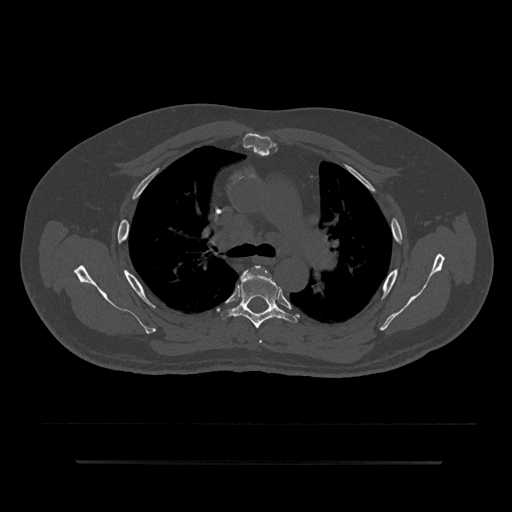
CT including the spine, one axial slice. Slice 579 of 797 in the series (ordered by position). Reconstruction kernel Br40s/3. 120 kVp. Bone window (W 1800 / L 400 HU). 512 × 512 image matrix, field of view 464 × 464 mm. Patient: male, 59 years. From the clinical record (not read from this slice): primary cancer: bile ducts; vertebrae with lytic lesions (as recorded): T10.
Outlined on this slice (semi-automatic segmentation, software-assisted and operator-edited):
- T4 vertebra: bounding box <253,266,267,343> (left, top, right, bottom; pixels)
- T5 vertebra: <225,270,297,329>